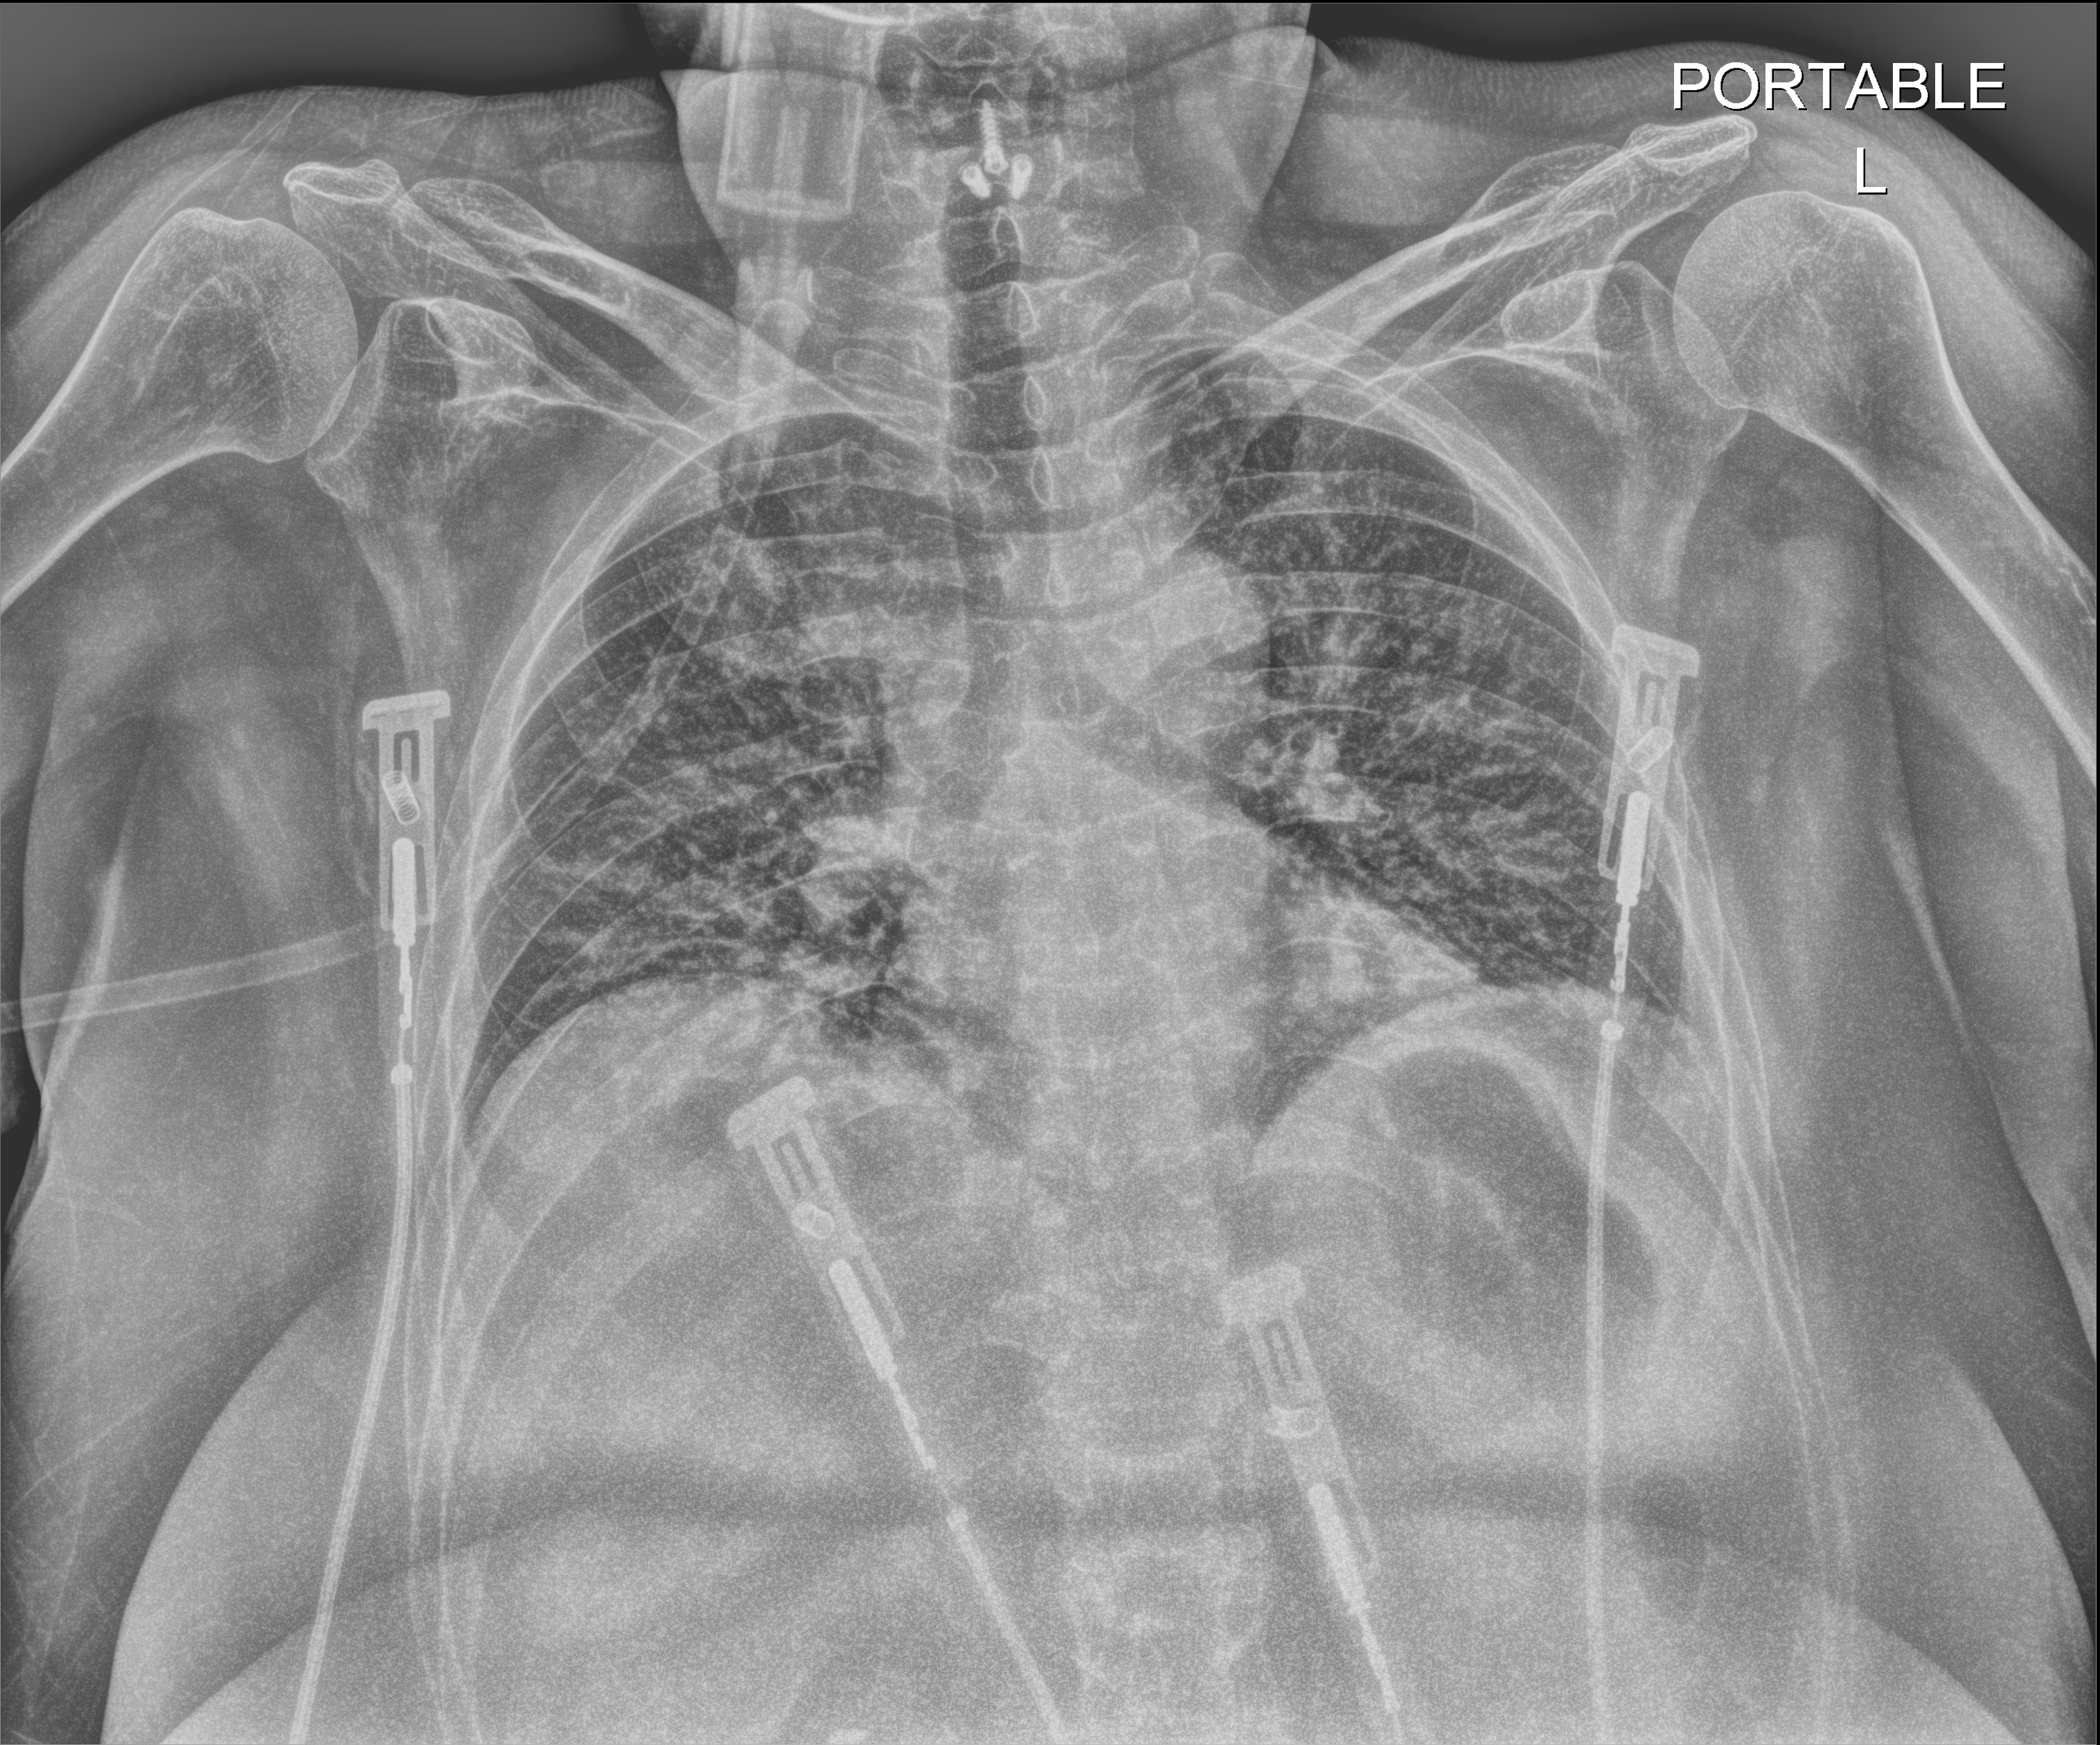
Chest radiograph (digital radiography), anteroposterior (AP) projection. Patient hospitalised with COVID-19; female, aged 18–59 years.
From the hospital-stay record, not from the radiograph (when in the stay this image was taken is not recorded): admitted to intensive care during this hospital stay: yes; mechanically ventilated during this hospital stay: no.